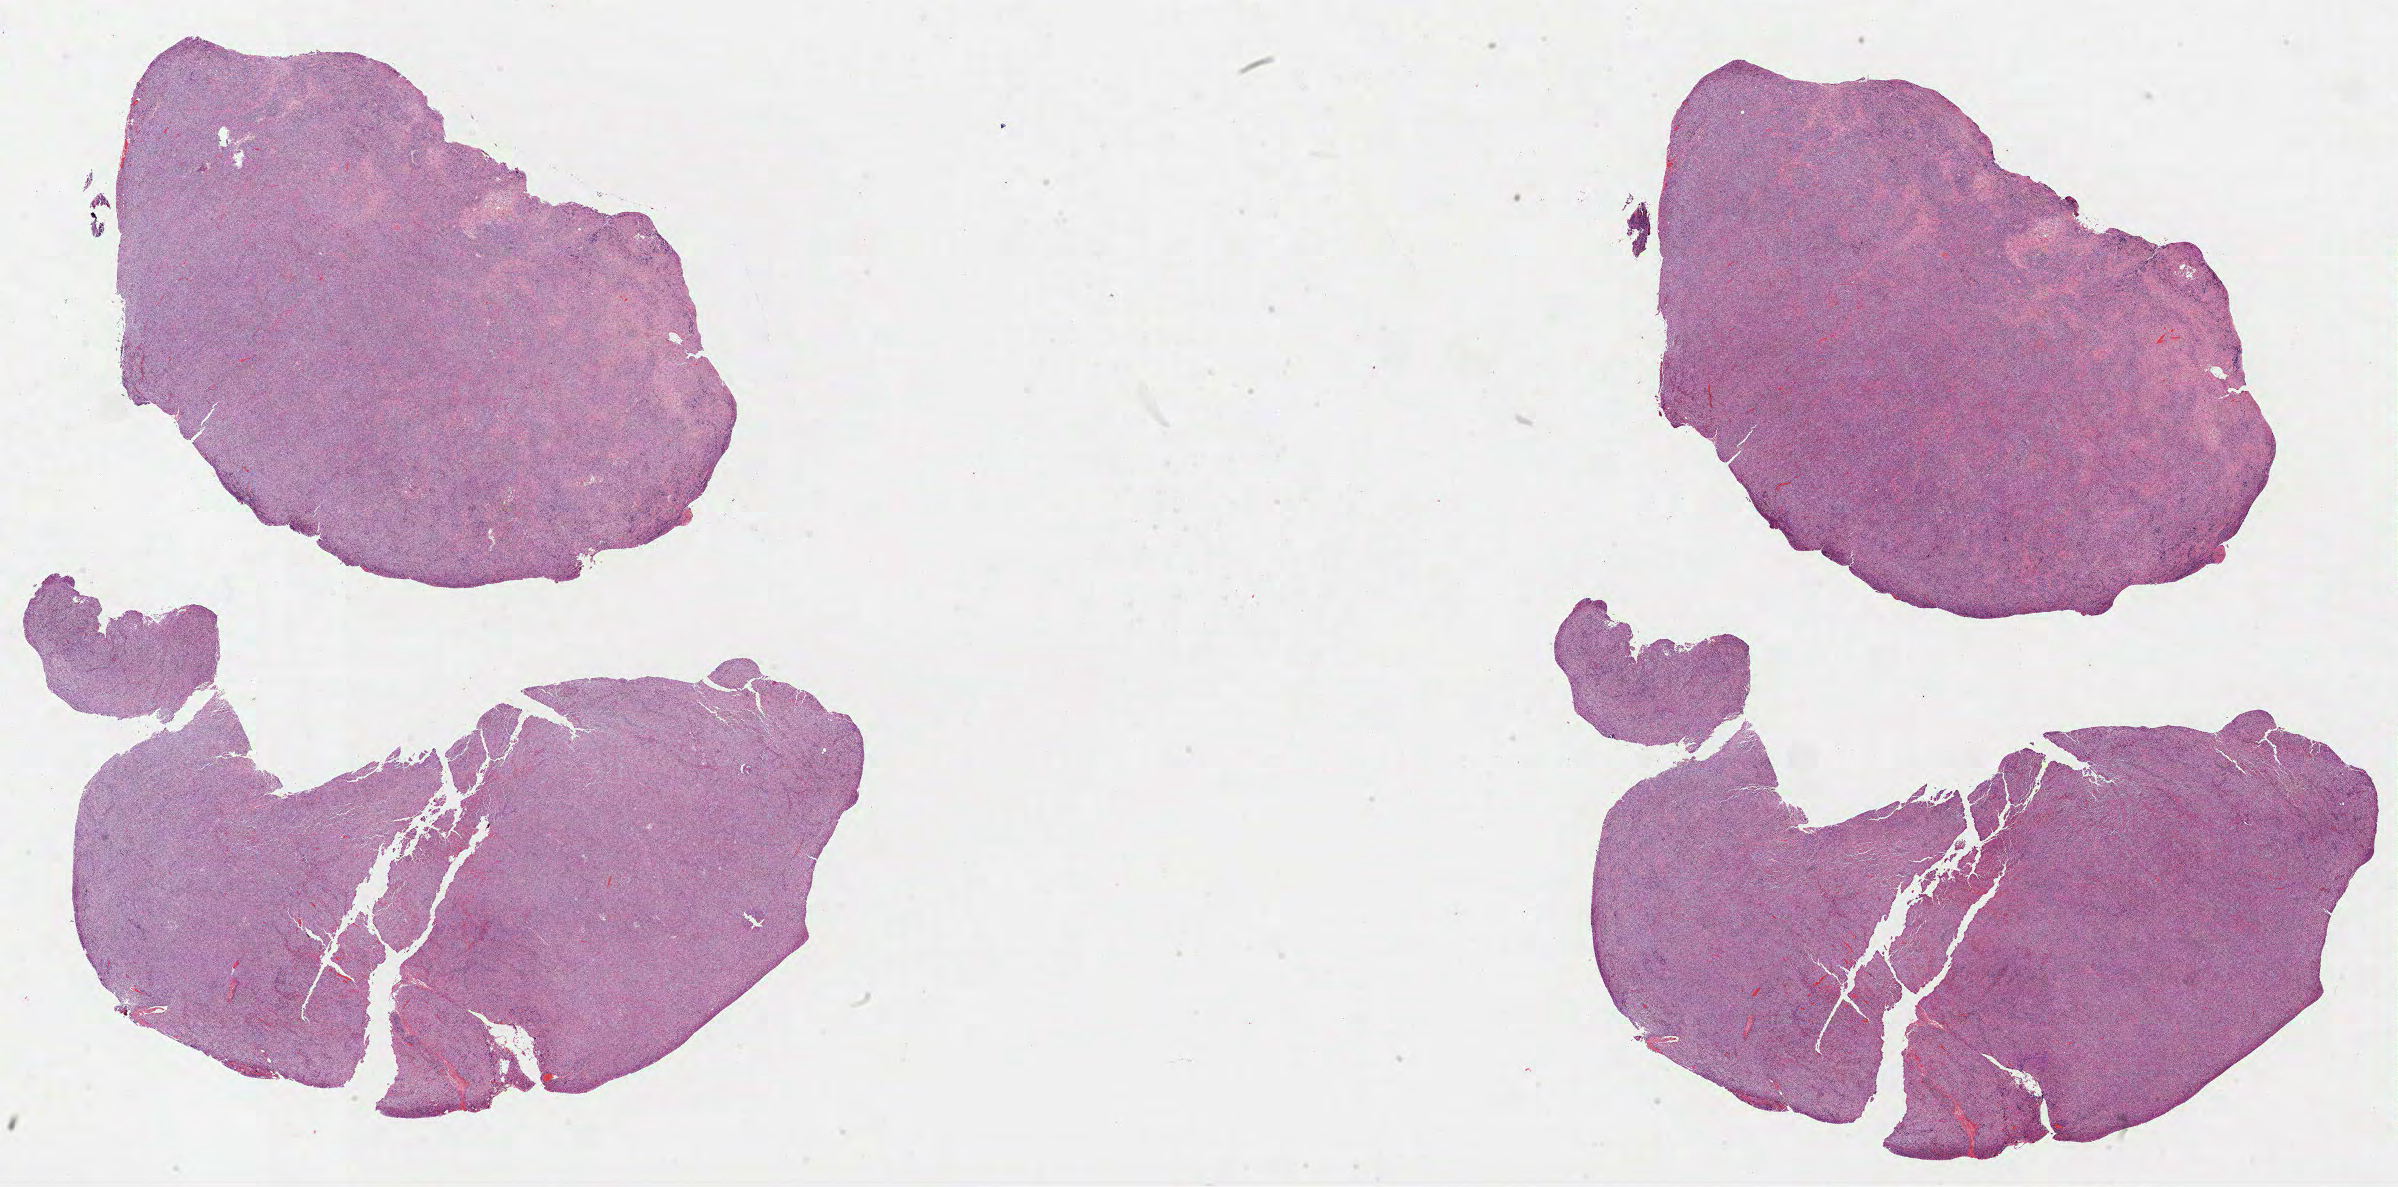
Digitized Hematoxylin and eosin (H&E) stained tissue section (whole slide) — low-resolution overview of the scanned area, about 38.7 x 19.1 mm; FFPE section; primary tumour sample from the lymphoid tissue. Male, age 69 years at initial diagnosis.
Pathologic diagnosis: Diffuse large B-cell lymphoma, NOS (intra-abdominal lymph nodes).